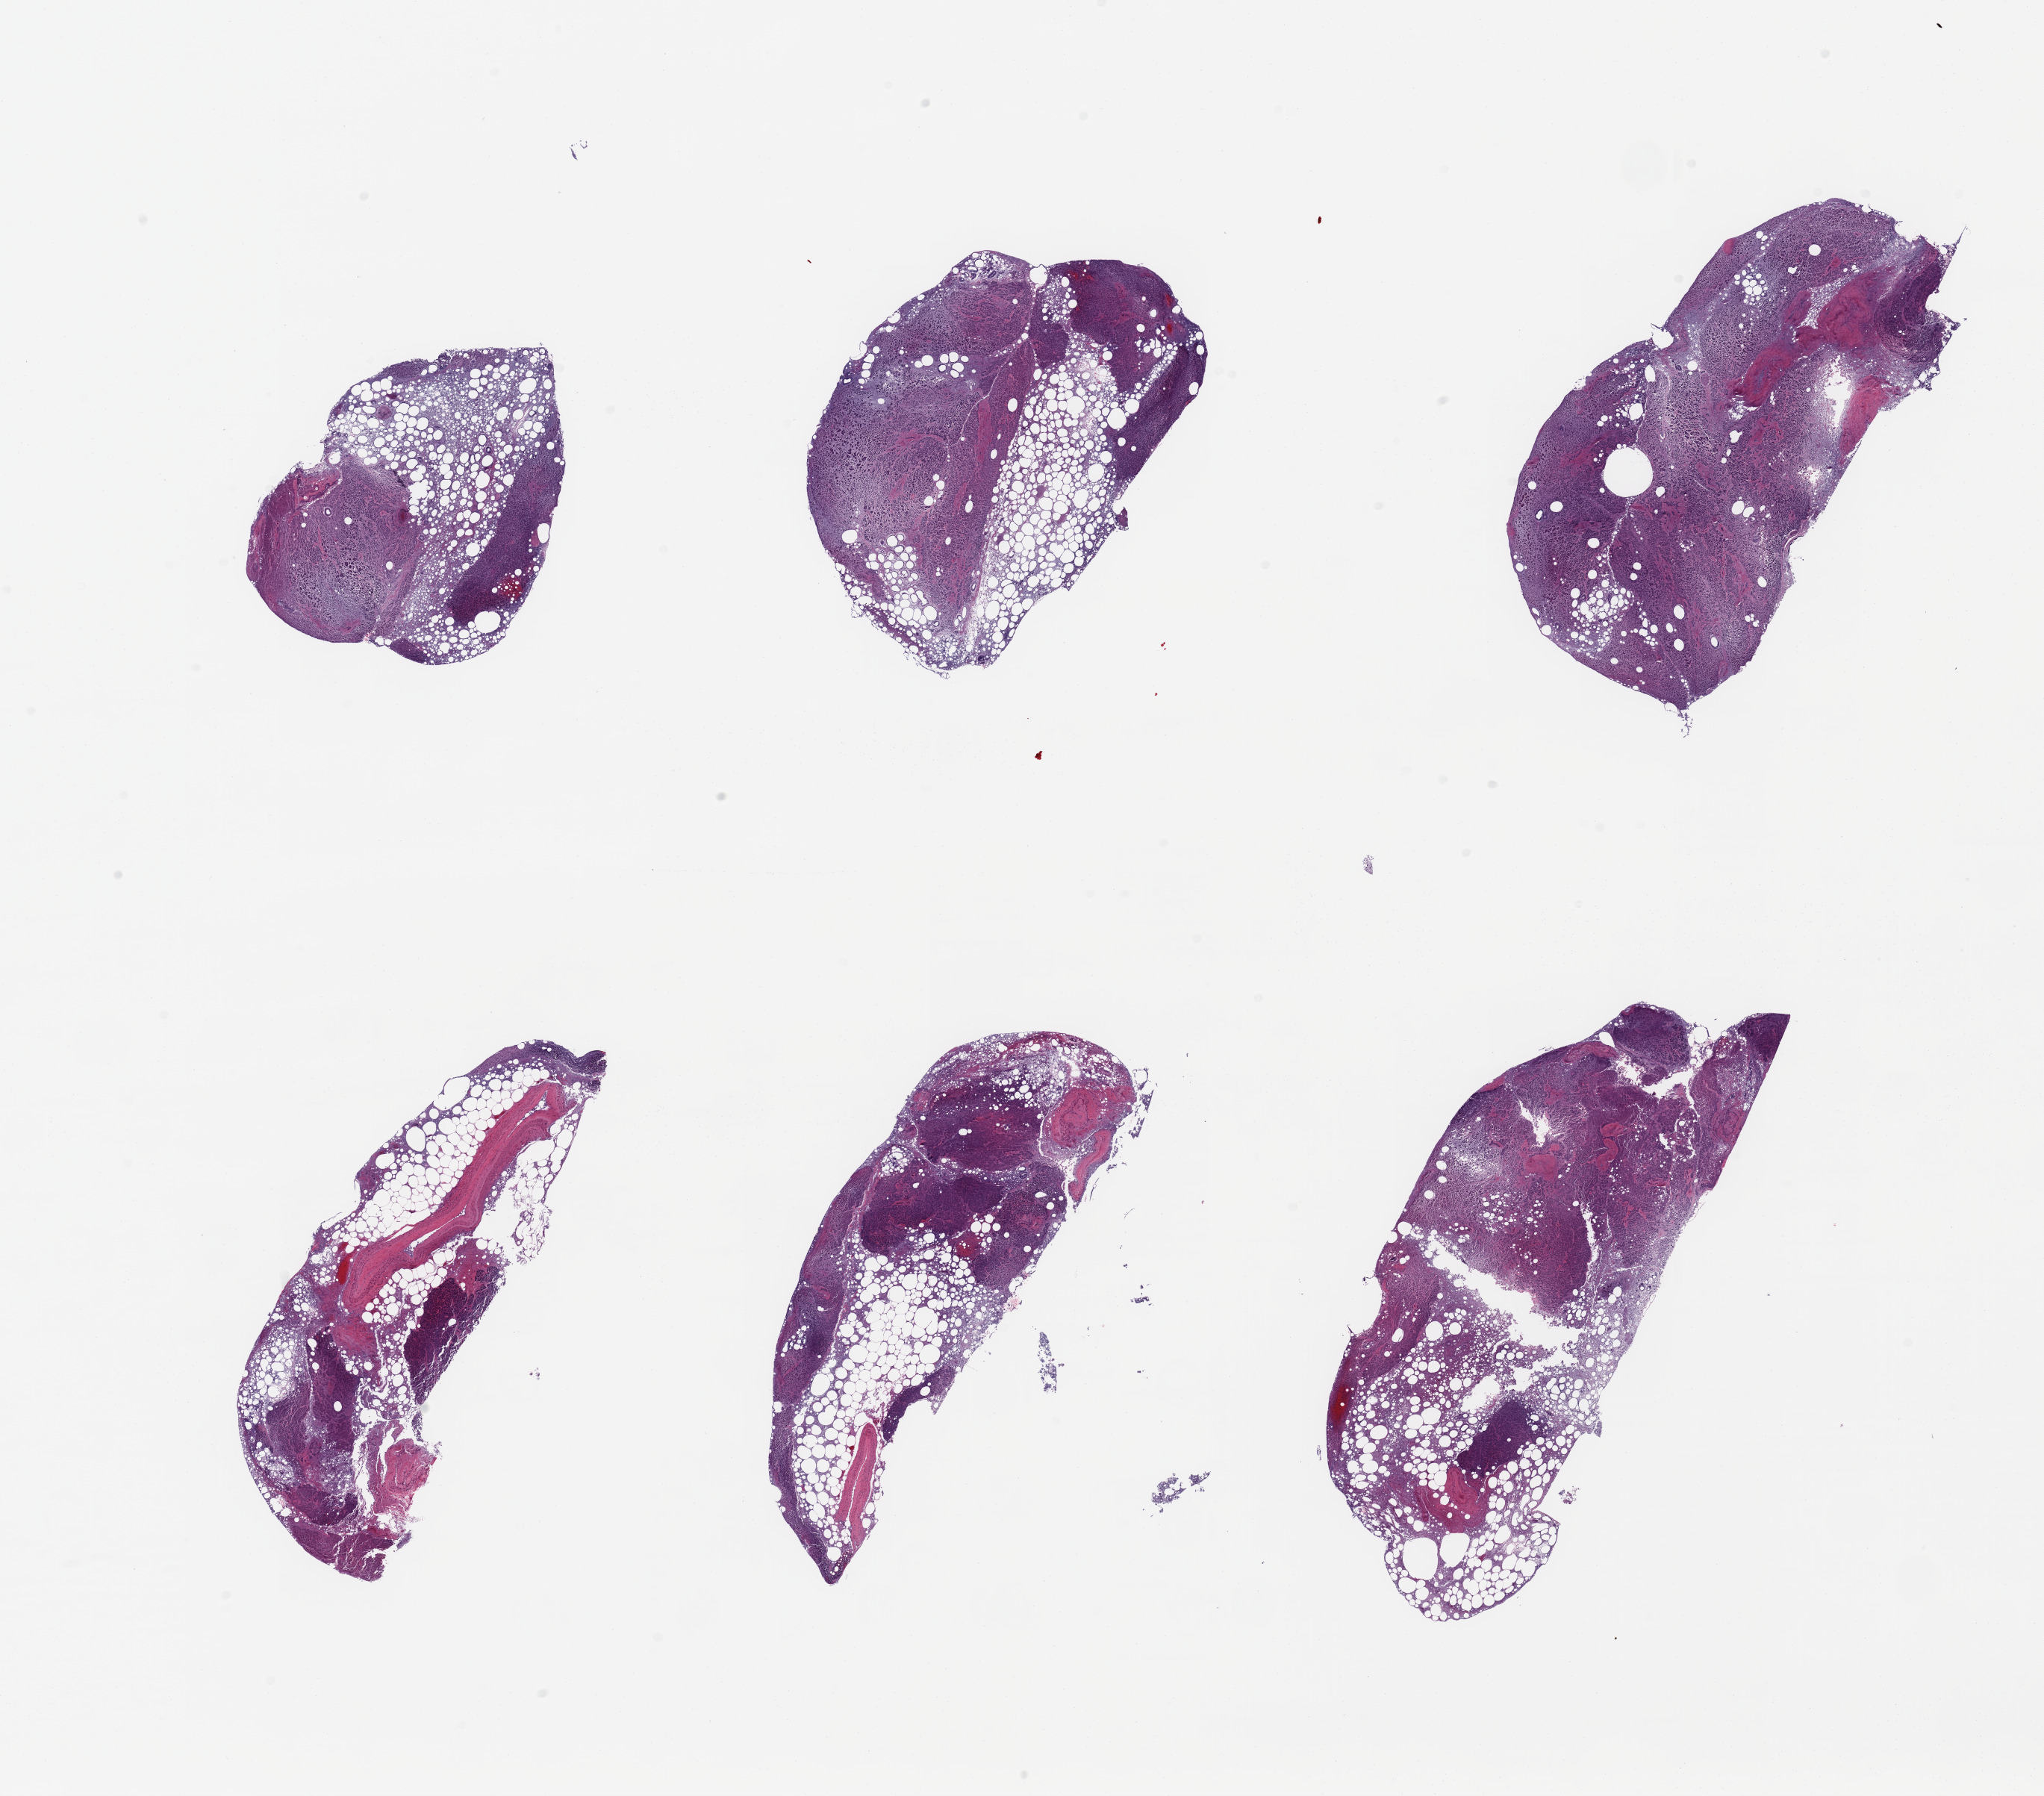
Whole-slide image, haematoxylin and eosin stain — low-resolution overview of the scanned area, about 21.7 x 19.0 mm (slide scanned at 20x), PAXgene-fixed, paraffin-embedded tissue, sampled site (target tissue): pancreas, tissue donor sample. Male donor.
Reviewer comment on this tissue sample: 6 pieces, advanced saponification.